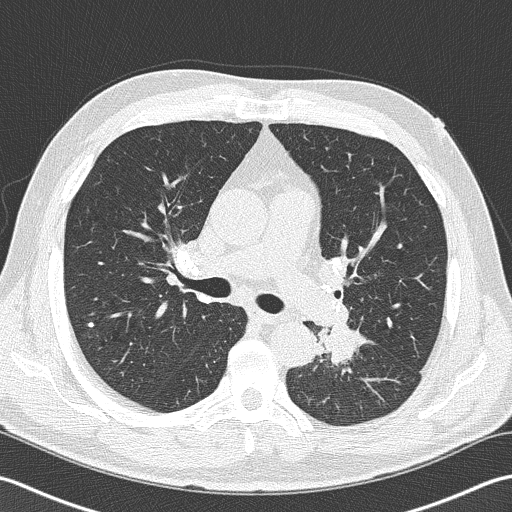
Chest CT (low-dose screening protocol), one axial image, second annual screen, lung window (W 1500 / L -600 HU), 2 mm slice thickness, lung (sharp) reconstruction kernel (B50f), 120 kVp, 512 × 512 image matrix. Male participant, aged 57 years at enrolment. Former smoker at enrolment.
- Expert reader's lesion annotation, box from (x=294, y=310) to (x=374, y=385) px.
- The exam's reader record, not a measurement of the box and not confirmed to be the same lesion: non-calcified nodule or mass ≥4 mm, left lower lobe, 40 × 30 mm, spiculated (stellate) margins, soft tissue attenuation, pre-existing on the prior screen: no.
- Later outcome: lung cancer diagnosed 9 days after this screen — squamous cell carcinoma, NOS, left lower lobe, moderately differentiated (G2), stage IIIB (AJCC 6th edition), 38 mm at pathology.